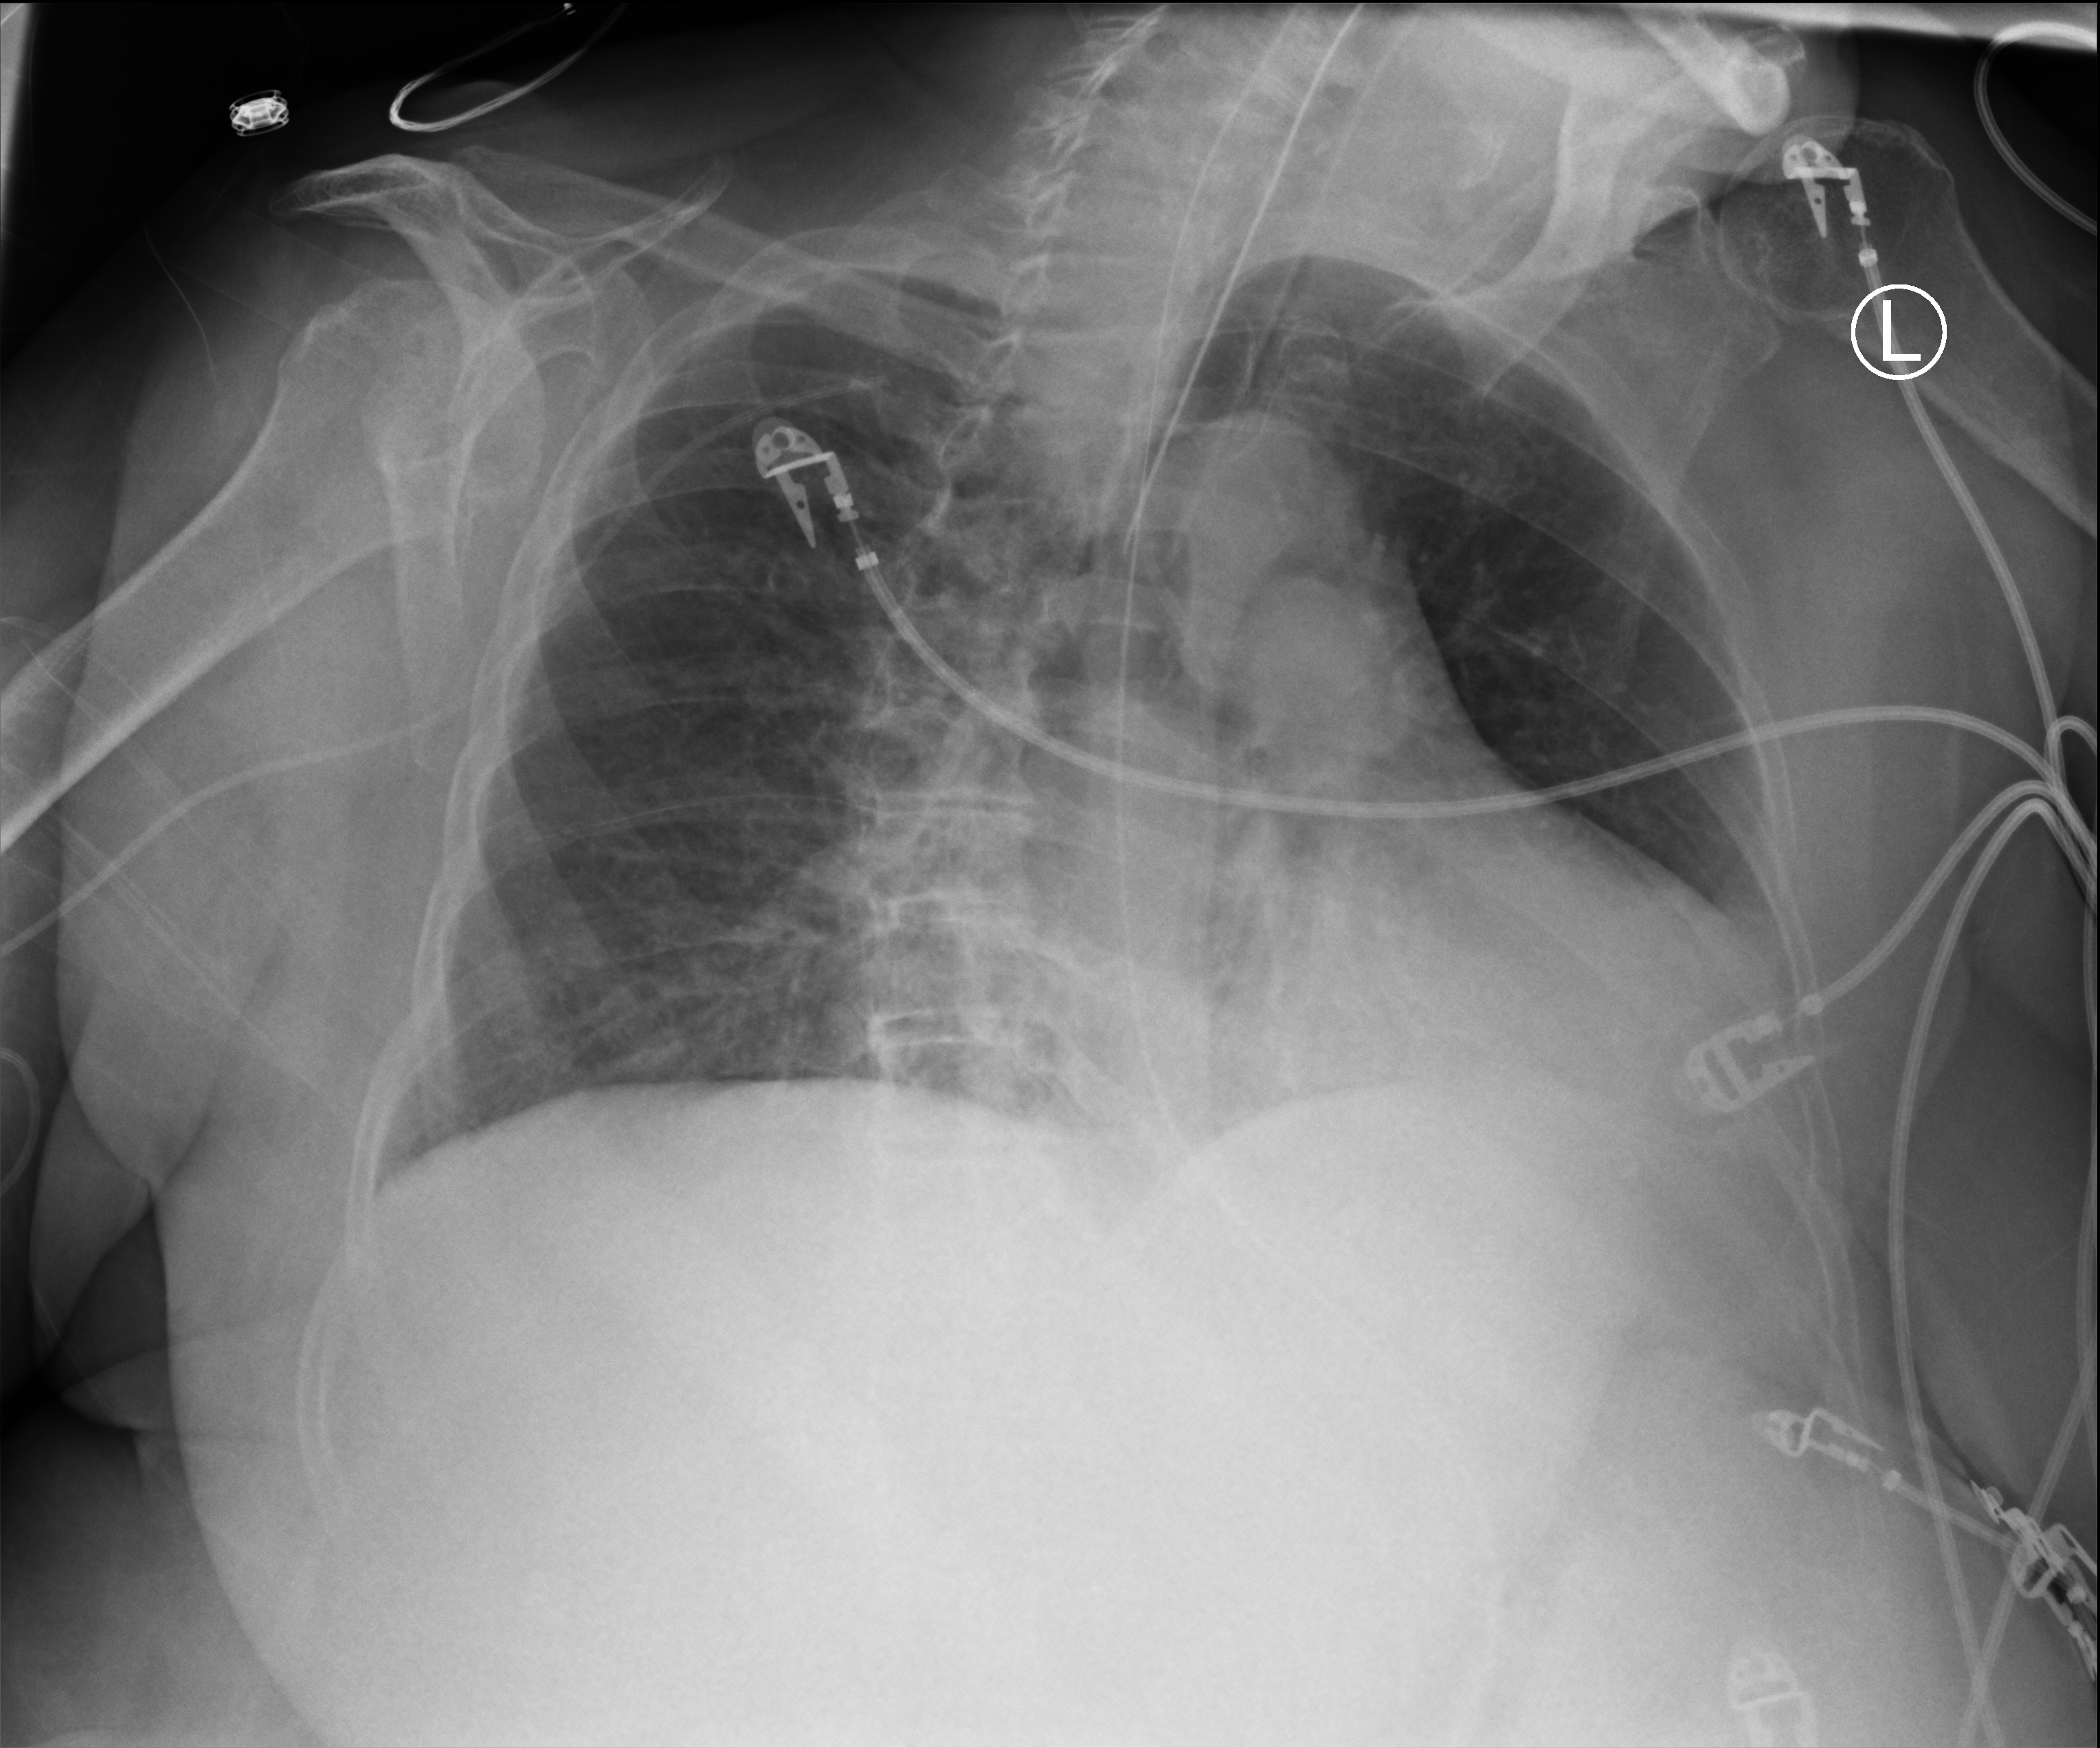
Chest X-ray (portable); anteroposterior (AP) projection. Patient hospitalised with COVID-19; female, aged 75–90 years.
Hospital-stay facts (about this admission, not read from this image; timing relative to this image not recorded): mechanically ventilated during this hospital stay: yes; admitted to intensive care during this hospital stay: yes; chronic kidney disease (admission record): no.